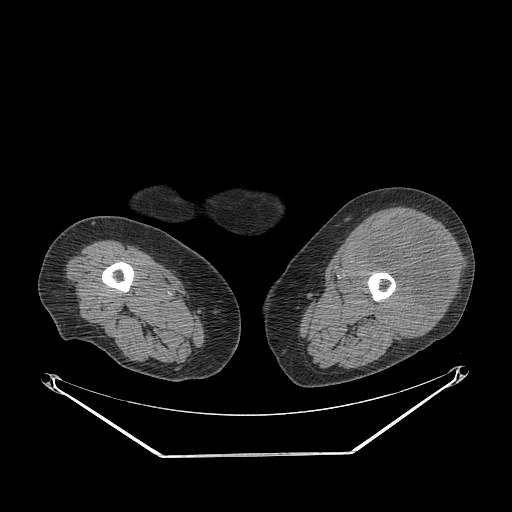
CT of an extremity soft-tissue mass (from a PET/CT study), one axial slice; position 221 of 267 along the scan axis; reconstruction kernel STANDARD; soft-tissue window (W 400 / L 40 HU); 3.75 mm slice thickness; 512 × 512 image matrix. Female patient. From the clinical record (not read from this slice): histological type: undifferentiated – high grade; grade: high; site of the primary tumour: left thigh.
Annotated regions visible in this slice (expert contour drawn on MRI and transferred to this co-registered scan by the dataset authors):
- gross tumour volume including surrounding oedema: bounding box [x1, y1, x2, y2] px = [356, 217, 453, 336]
- gross tumour volume (mass): [356, 217, 453, 336]